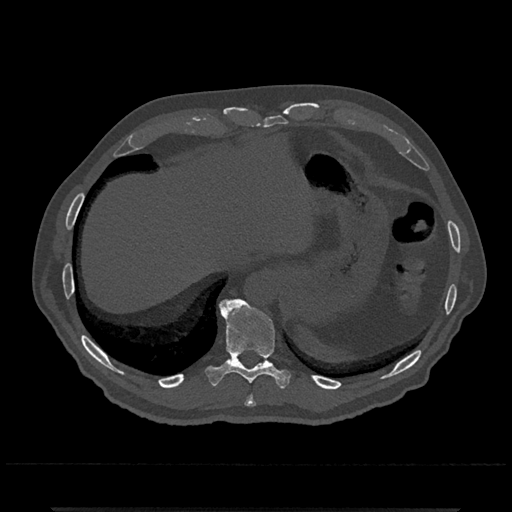
CT including the spine, one axial slice. Position 553 of 797 along the scan axis. 120 kVp. Bone window (W 1800 / L 400 HU). 512 × 512 image matrix, field of view 393 × 393 mm. Patient: male, 67 years. From the clinical record (not read from this slice): primary cancer: prostate.
Annotated regions visible in this slice (semi-automatic segmentation, software-assisted and operator-edited):
- T10 vertebra: bounding box <205,298,291,389> (left, top, right, bottom; pixels)
- T11 vertebra: <230,358,238,359>
- T9 vertebra: <245,395,256,407>